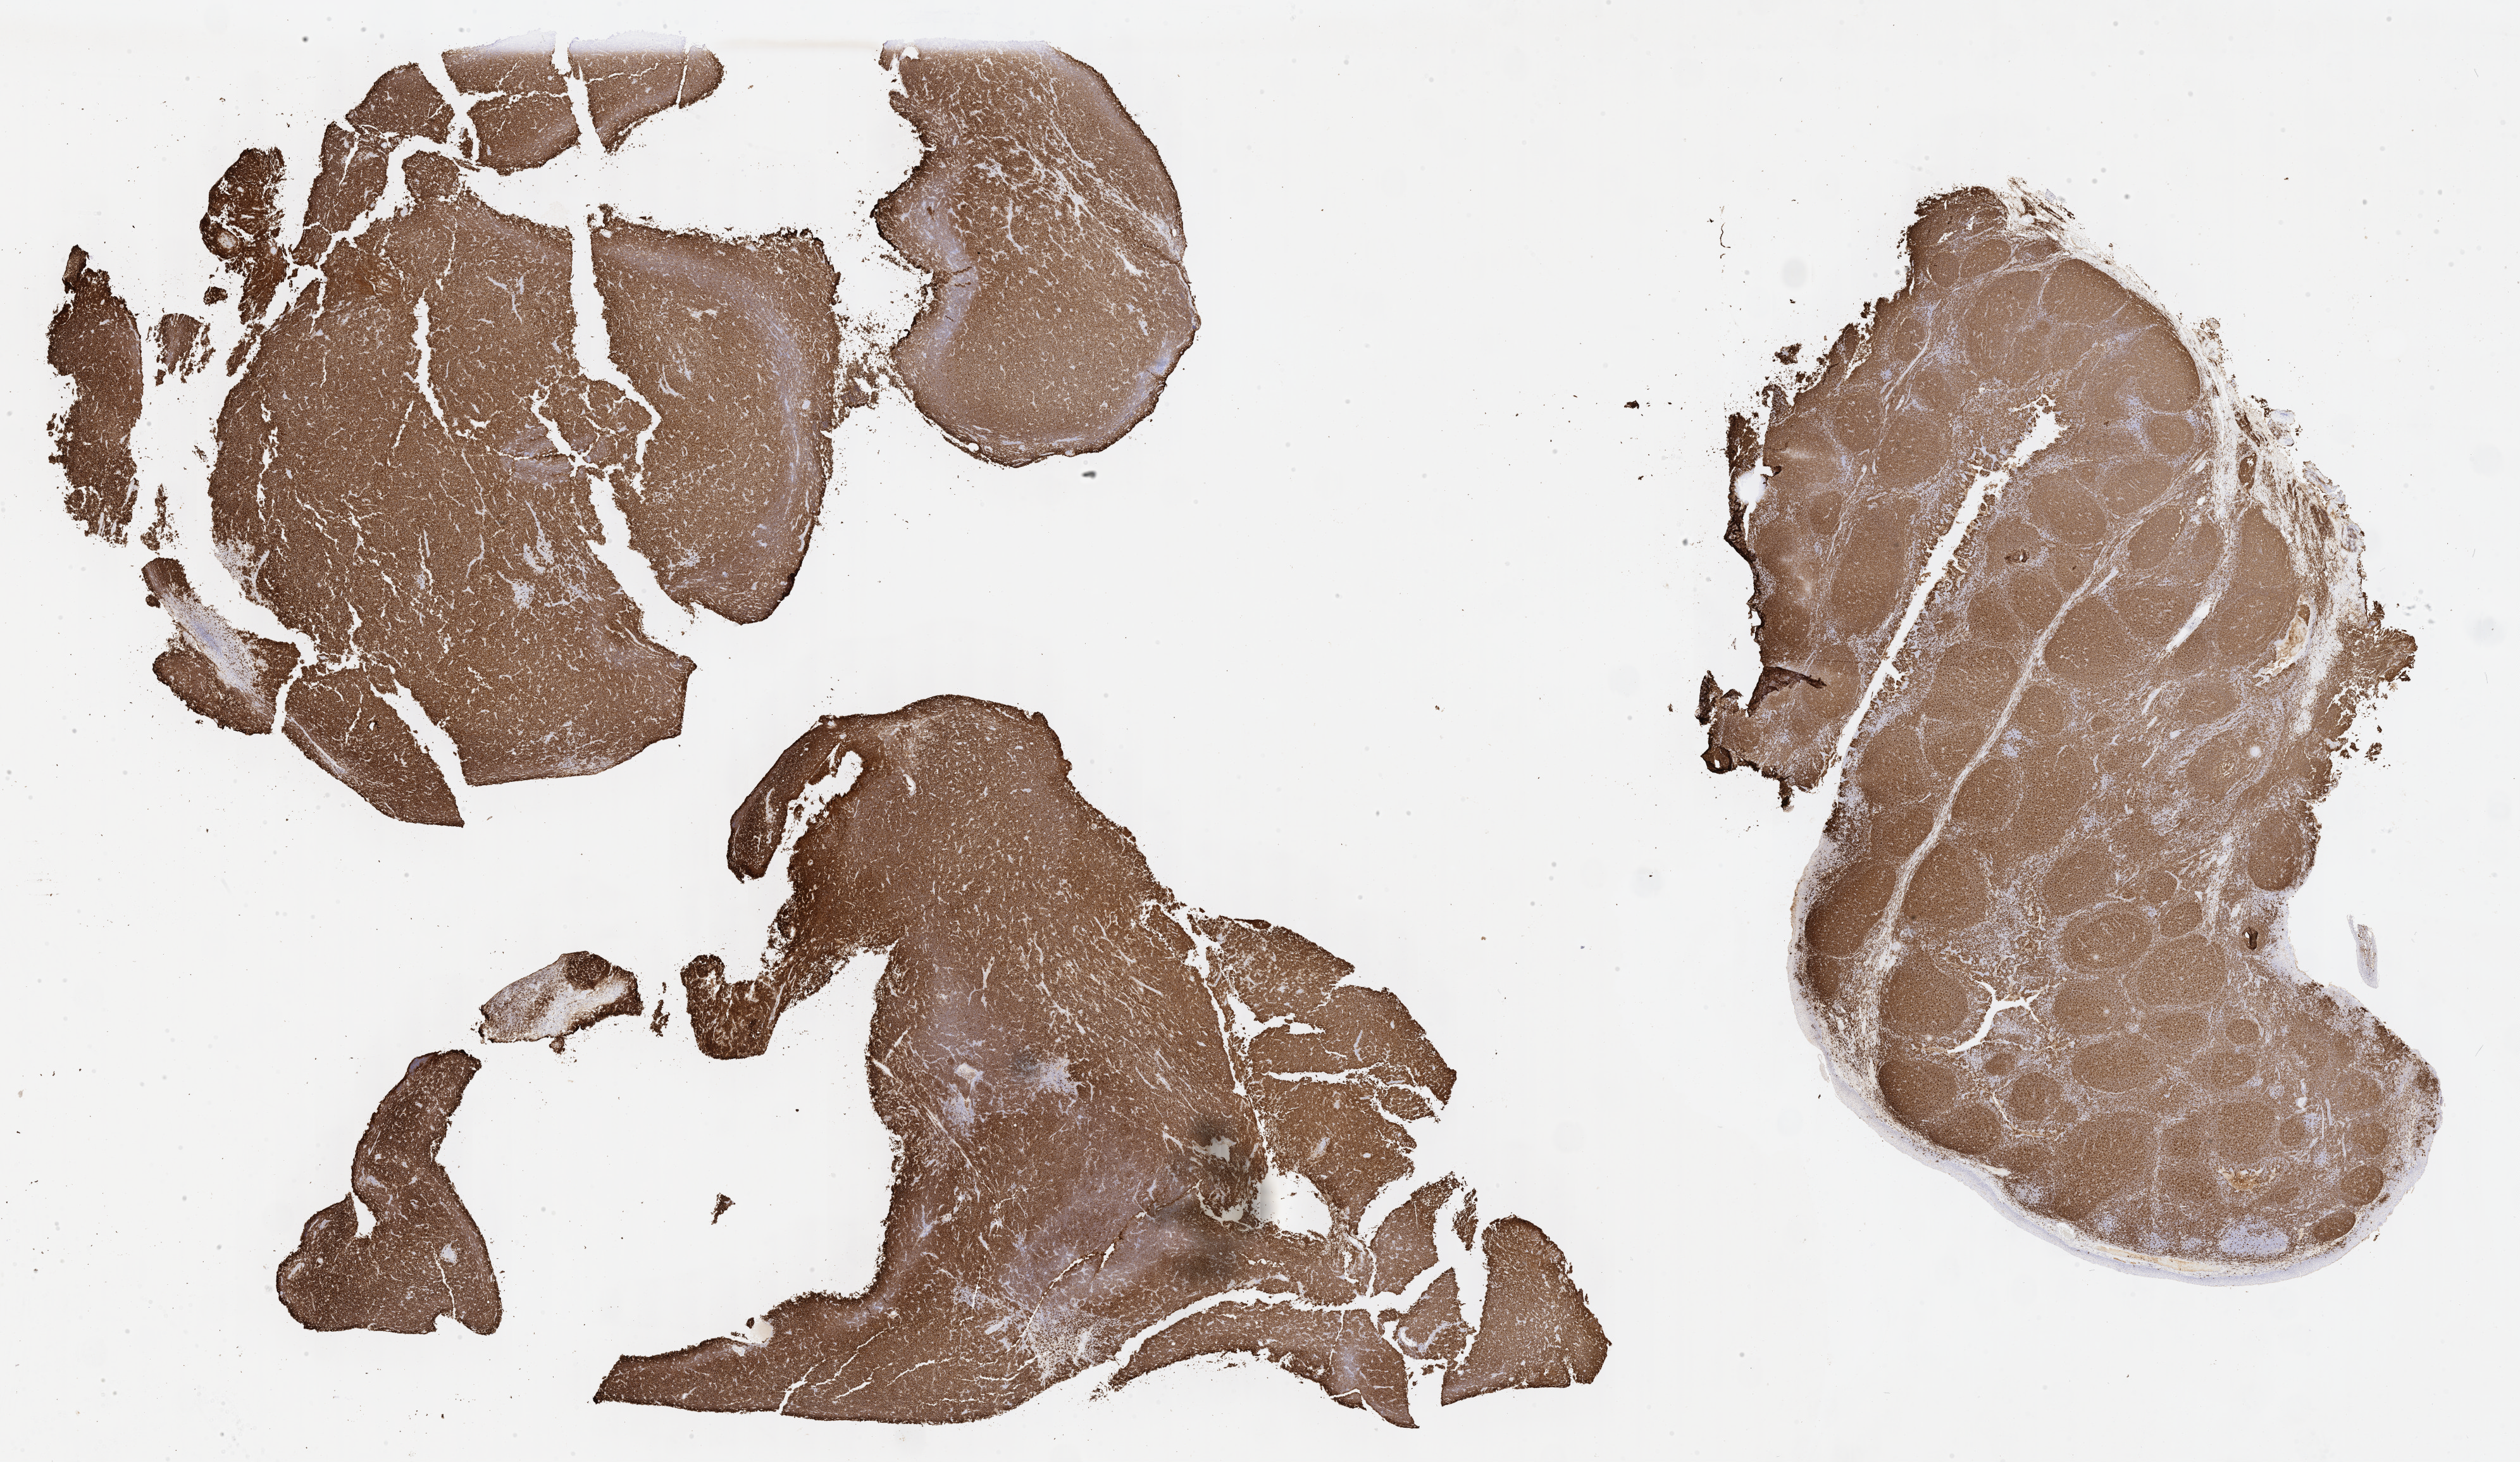
Immunohistochemistry (IHC) whole-slide image stained for CD20 — low-resolution overview of the scanned area, about 32.2 x 18.7 mm. Tumor tissue. Anatomic site: liver. Male patient, 45 years old.
Diagnosis: Diffuse large B-cell lymphoma, NOS.